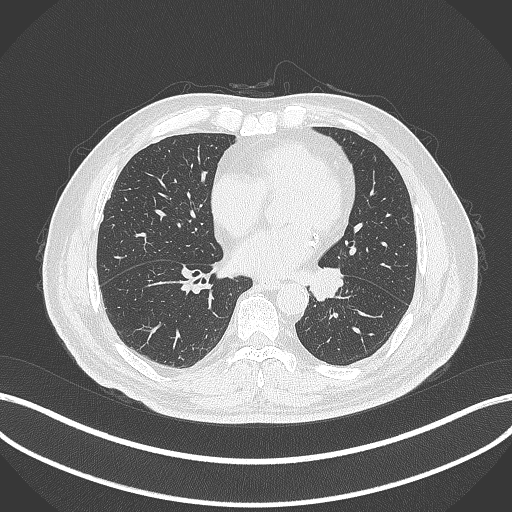
Chest CT, one axial slice; position 119 of 312 along the scan axis; reconstruction kernel B70f; lung window (W 1500 / L -600 HU); 512 × 512 image matrix, field of view 400 × 400 mm. Patient: male, 71 years. Case-level facts recorded for this patient, not image findings: clinical TNM (as recorded): T1b N0 M0.
Structures marked on this image (rectangle marked by the reading radiologist):
- lung tumour (recorded histology: squamous cell carcinoma): bounding box <305,264,350,304> (left, top, right, bottom; pixels)